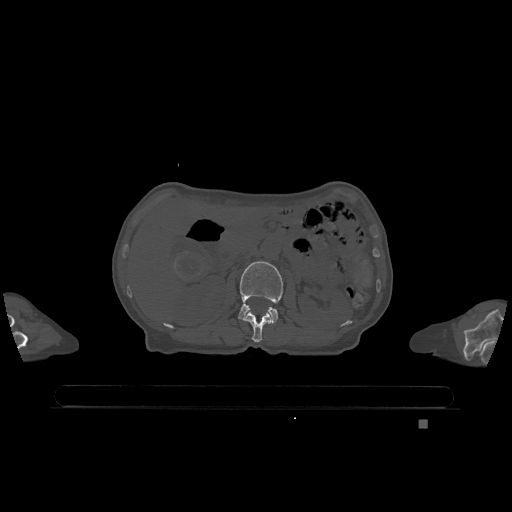
CT including the spine, one axial slice; slice 440 of 1317 in the series (ordered by position); bone window (W 1800 / L 400 HU); 512 × 512 image matrix. Female patient, age 74 years. Case-level facts recorded for this patient, not image findings: primary cancer: lung; vertebrae with lytic lesions (as recorded): T1, T4, T5, T6, L4, L5.
Annotated regions visible in this slice (semi-automatically segmented with operator editing):
- L1 vertebra: bounding box (x1, y1, x2, y2) in pixels: (244, 311, 272, 342)
- L2 vertebra: (238, 261, 284, 323)